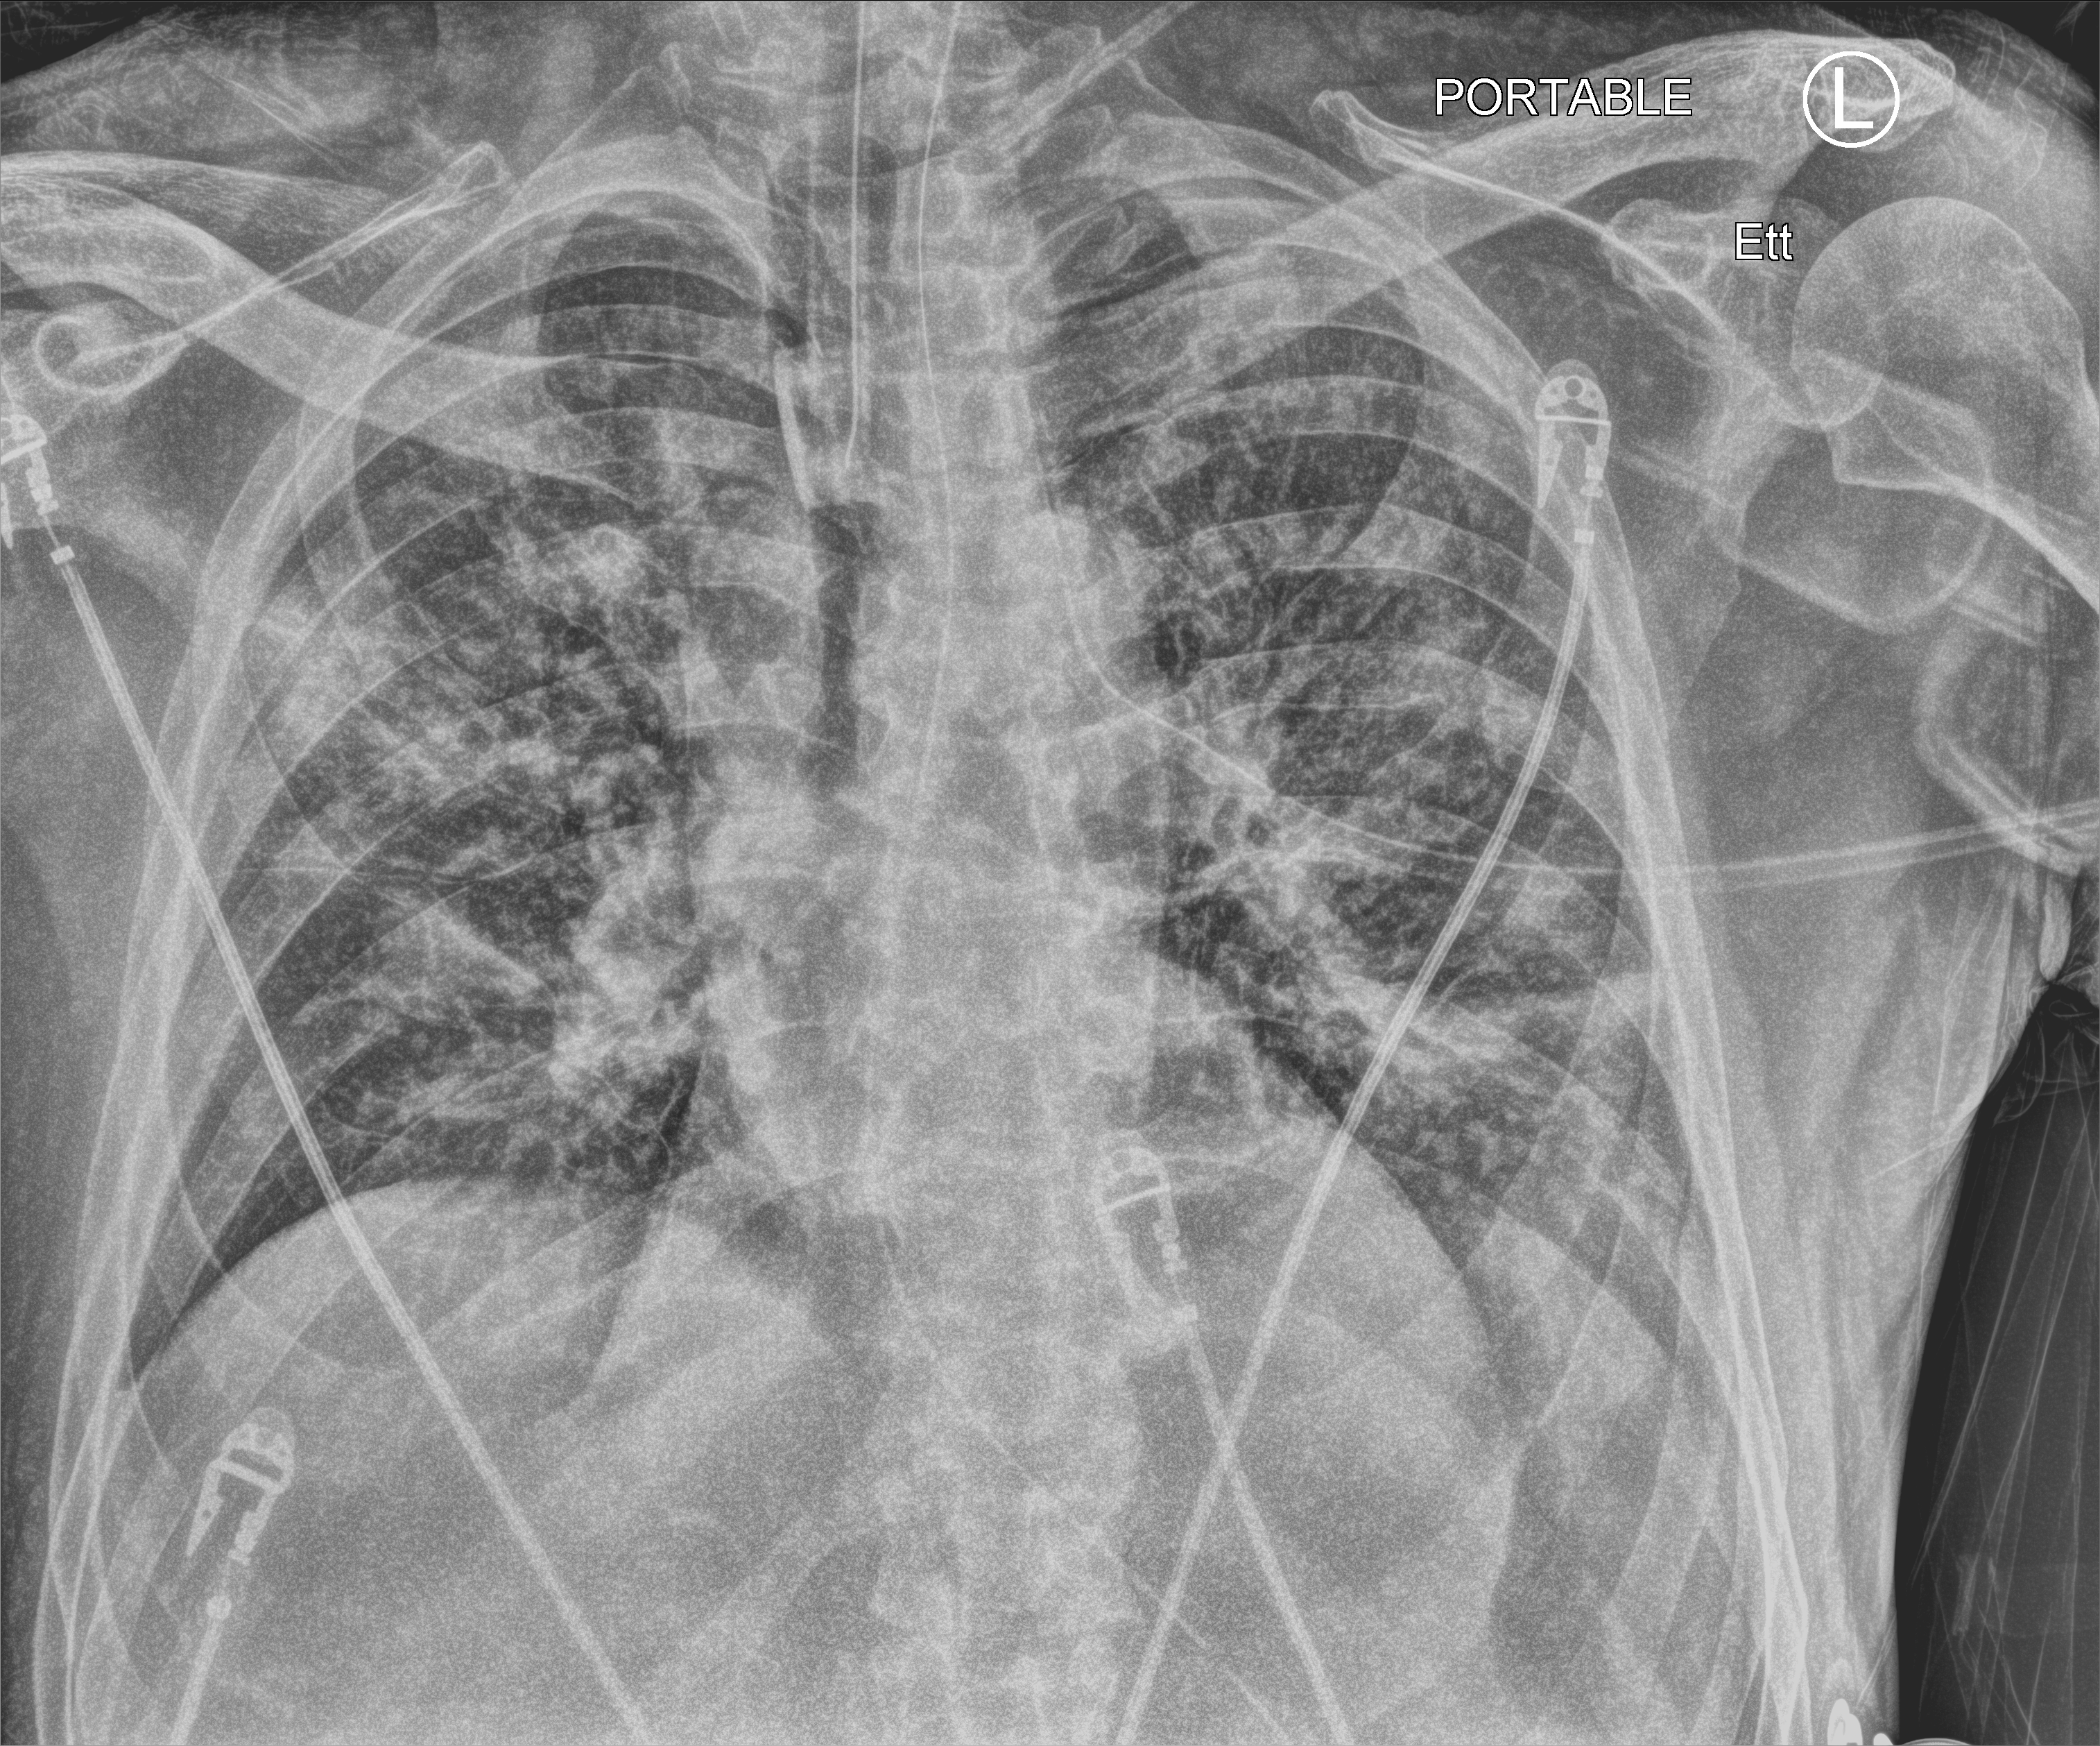
Portable chest radiograph. Patient hospitalised with COVID-19; male, aged 60–74 years.
From the hospital-stay record, not from the radiograph (when in the stay this image was taken is not recorded): chronic kidney disease (admission record): no.